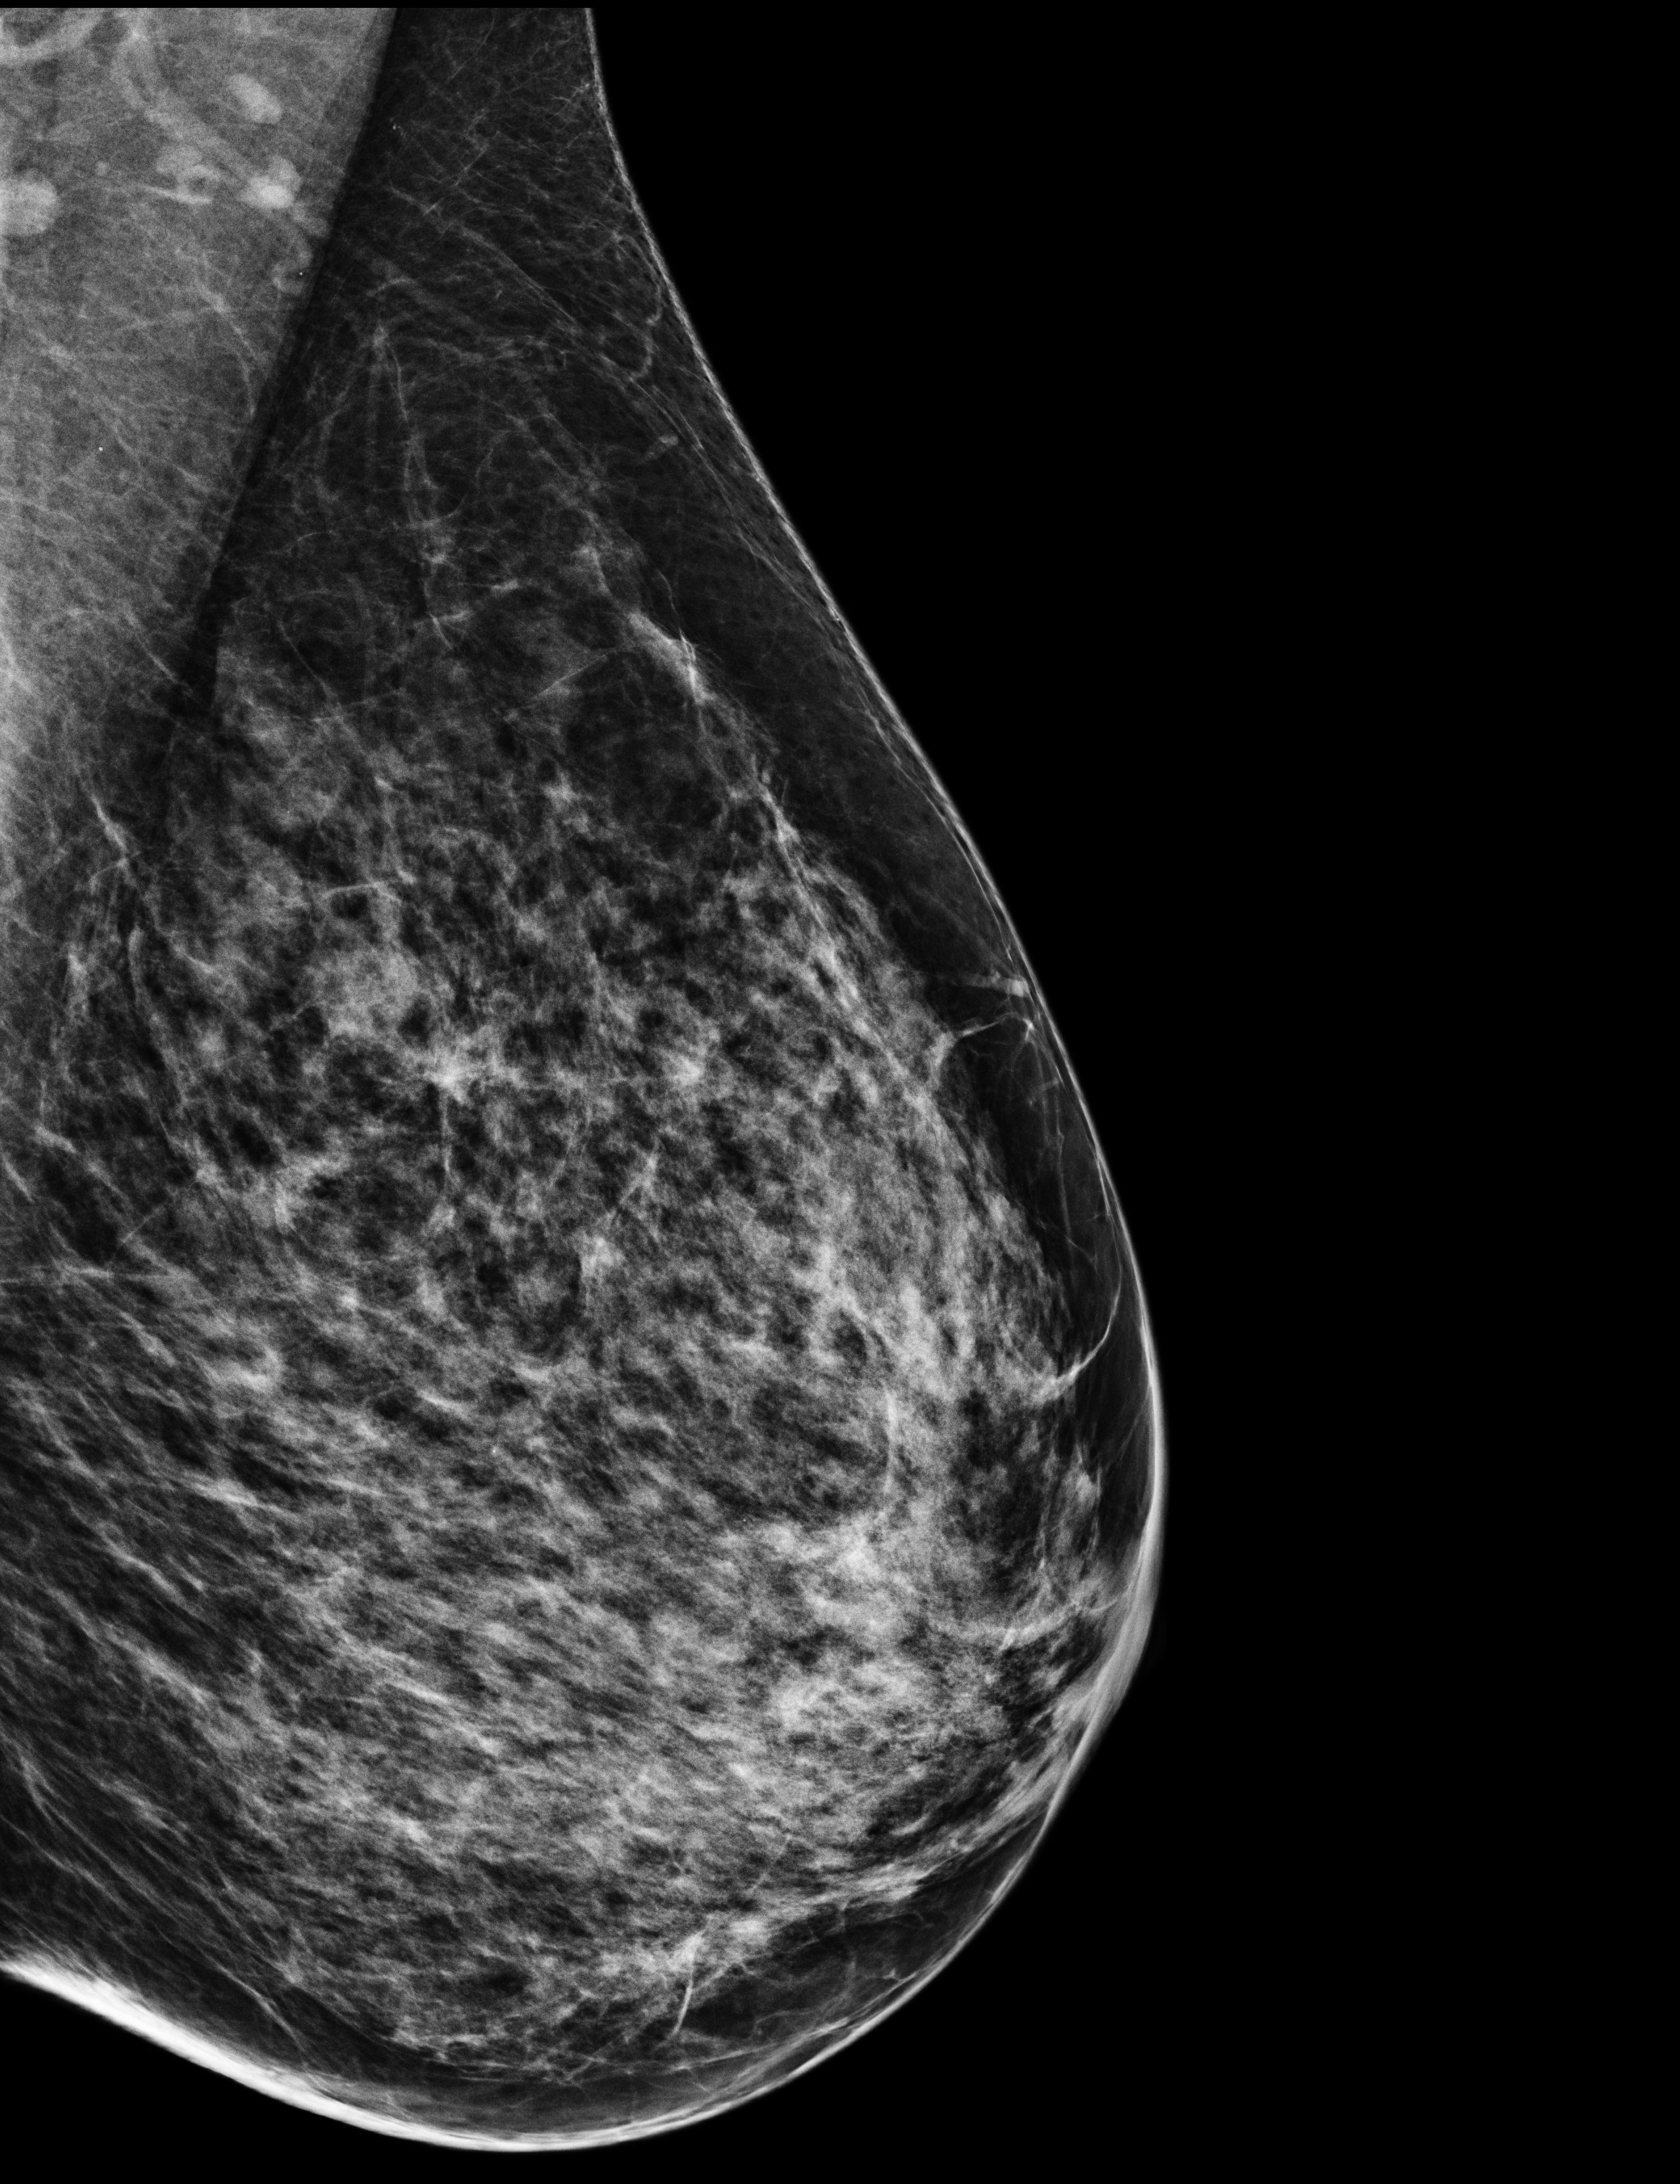
Screening examination, compressed breast thickness 54 mm. Female patient, age 59 years.
Image type: full-field digital mammogram. Breast: left. Projection: medio-lateral oblique projection.